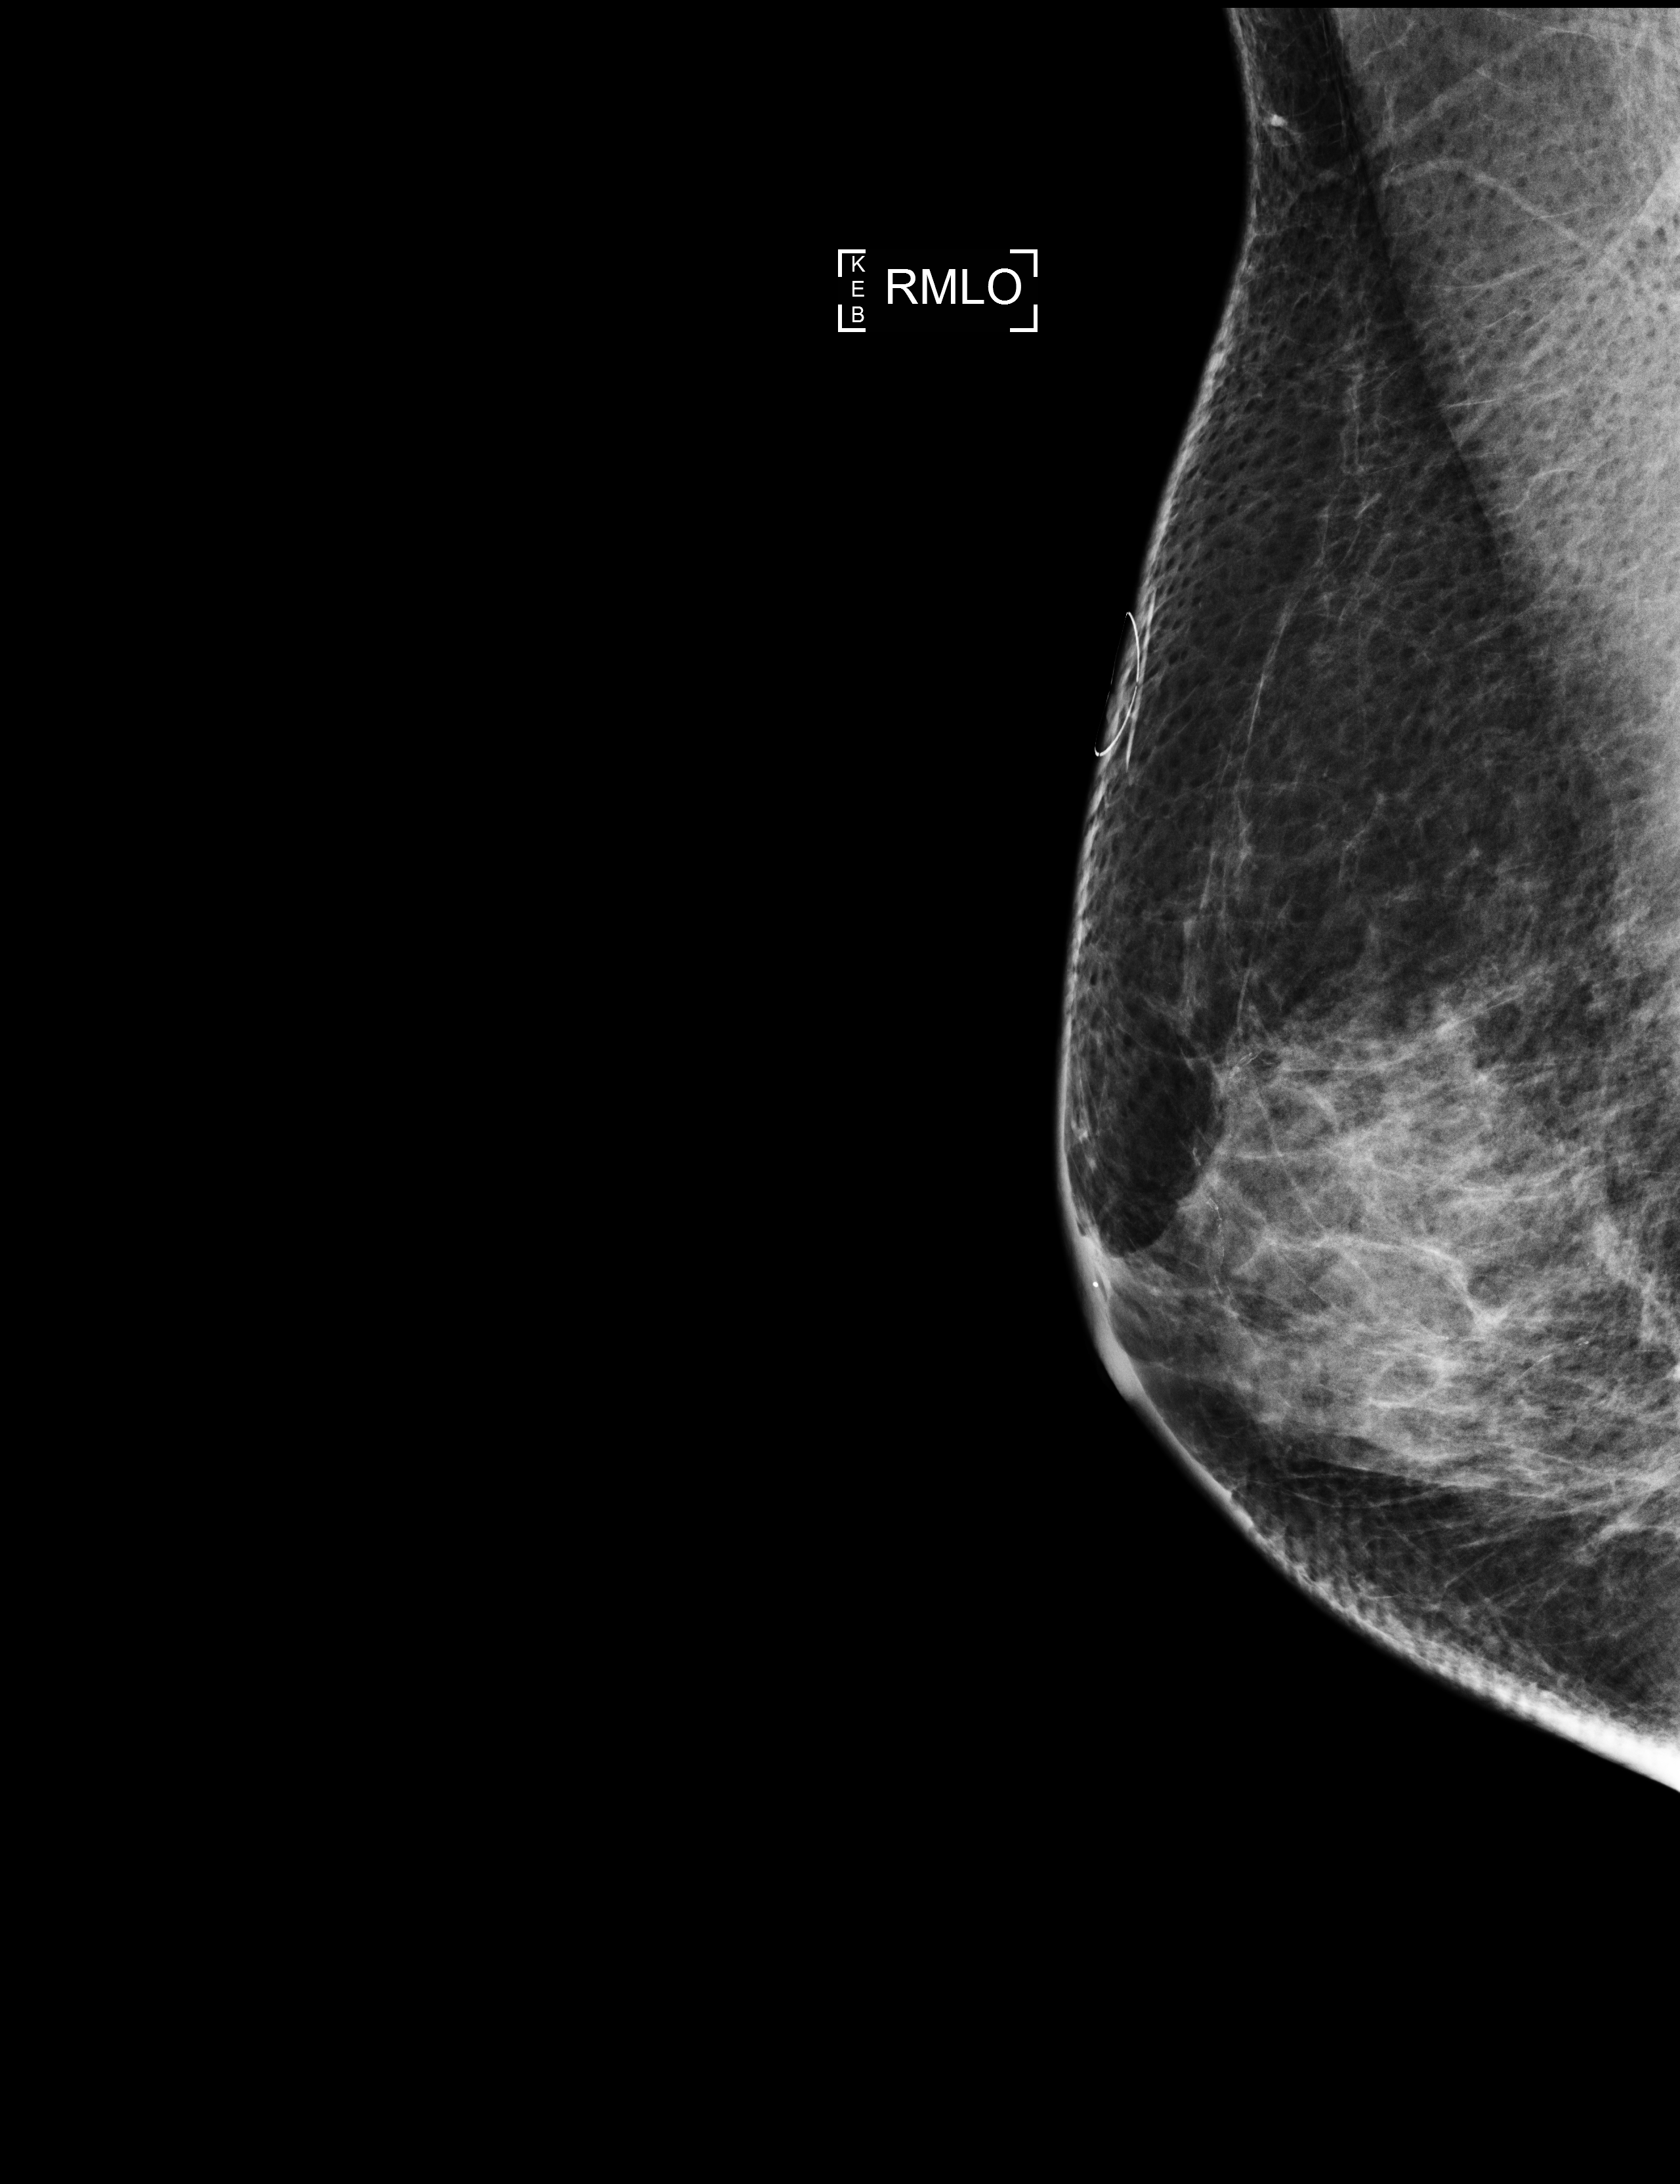
Annual screening mammography examination, system: Selenia Dimensions. Female patient, age 65 years.
Image type: full-field digital mammogram. Breast: right. Projection: mediolateral oblique (MLO) view.